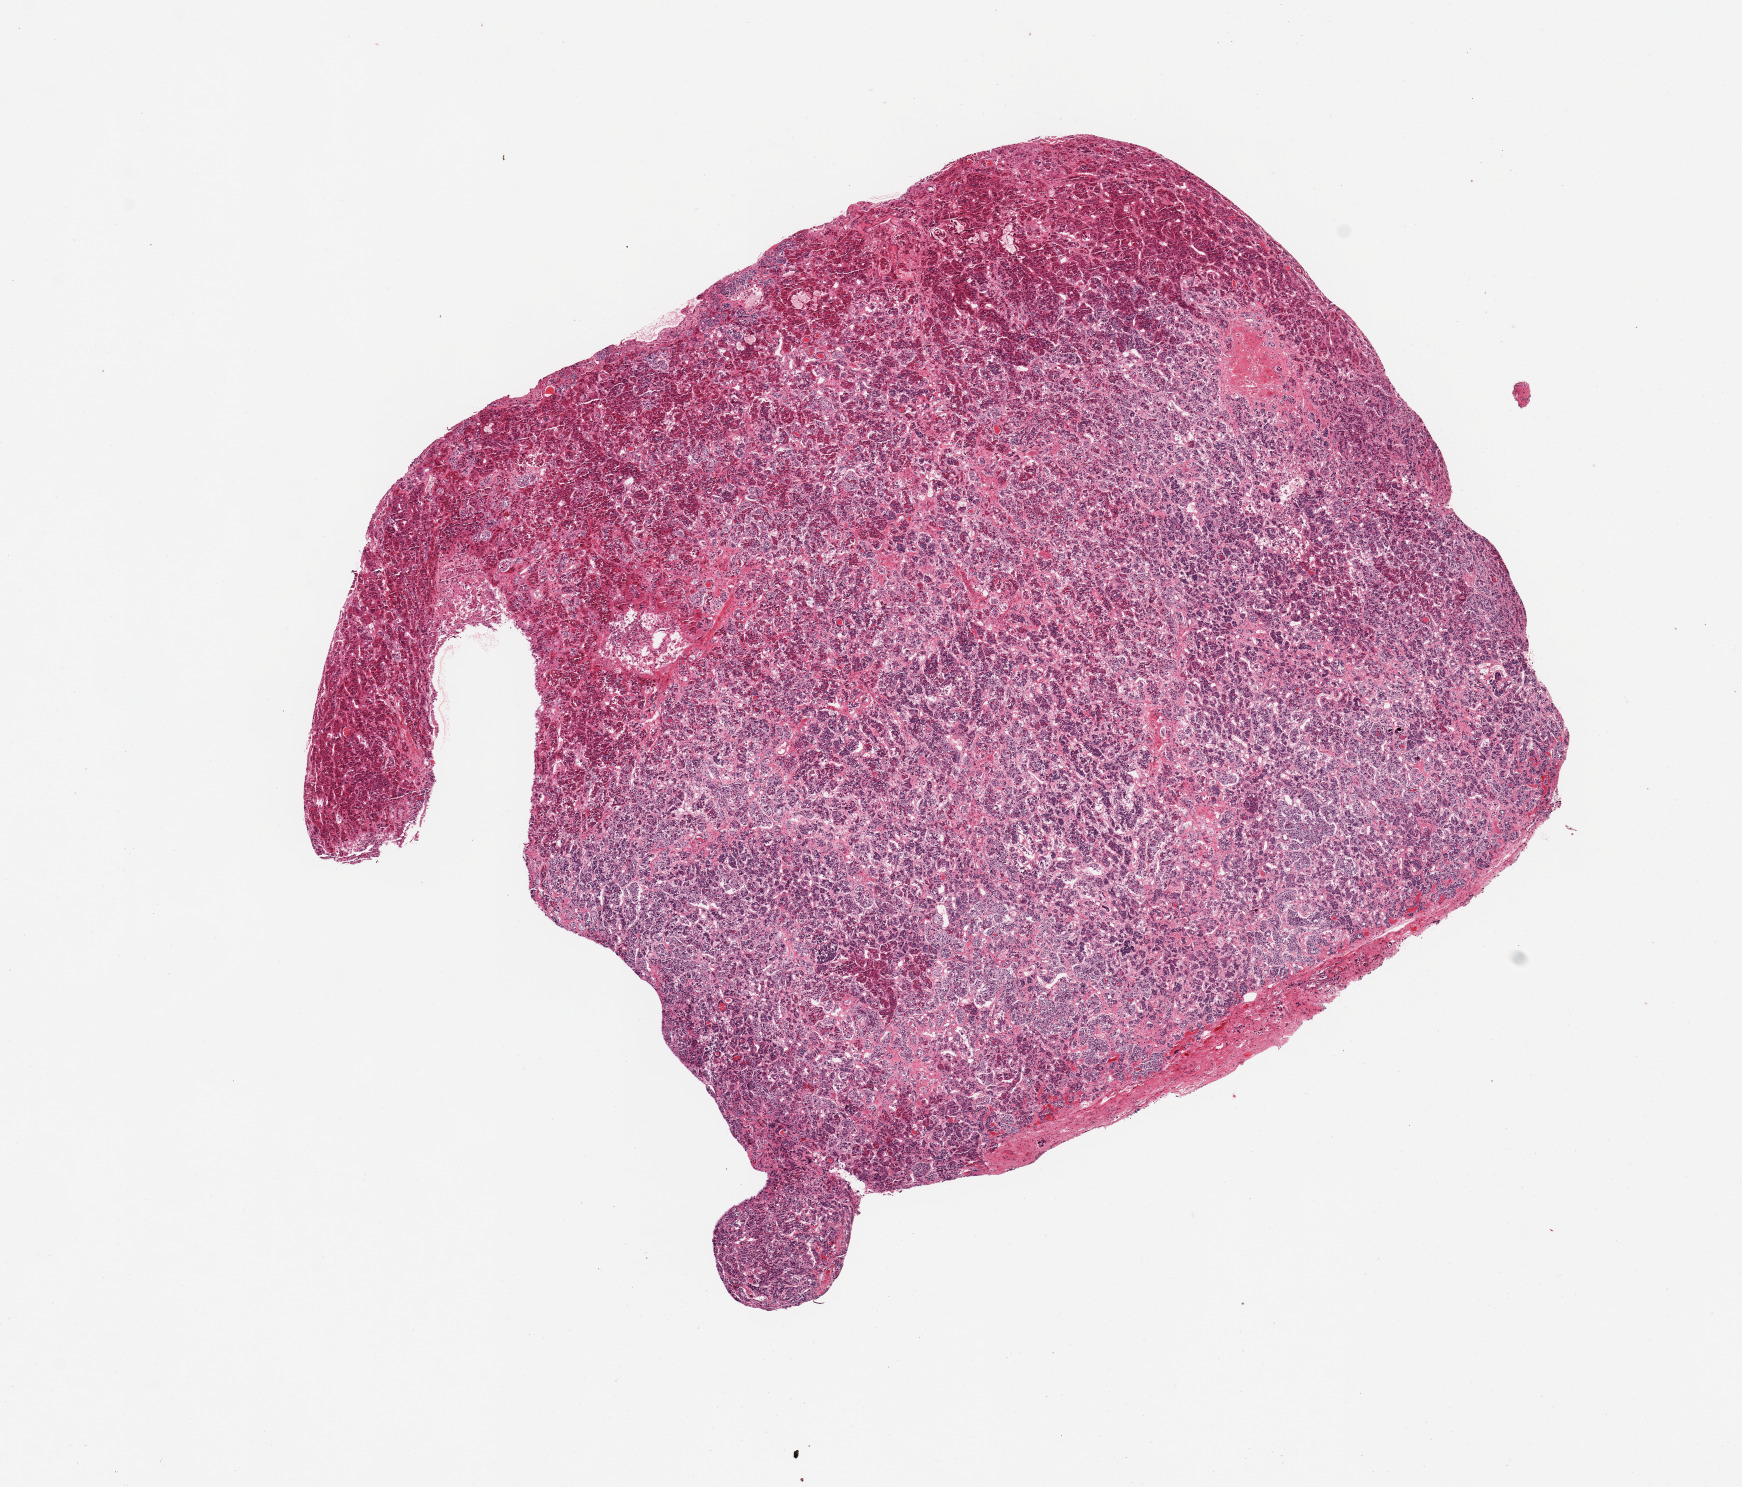
Haematoxylin and eosin whole-slide image, shown as a low-resolution overview of the whole scanned area (about 13.8 x 11.8 mm); PAXgene-fixed, paraffin-embedded tissue; target tissue: pituitary; tissue donor sample. Male donor.
* review note (as recorded): 1 piece, adenohypophysis only